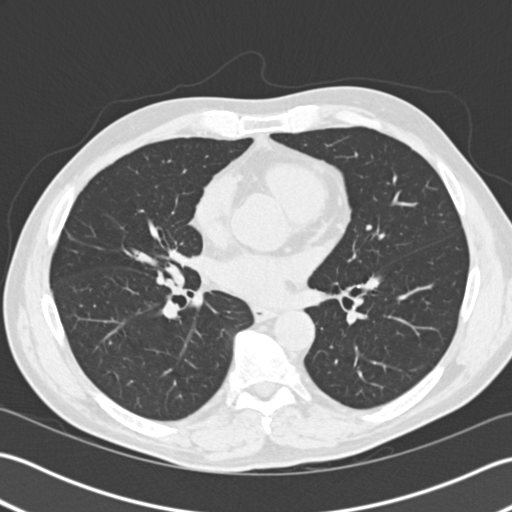
Chest CT (low-dose screening protocol), one axial image. Second screening round (one year after baseline). Lung window (W 1500 / L -600 HU). Slice 102 of 192 in the series. 512 × 512 image matrix. Male participant, aged 57 years at enrolment. Former smoker at enrolment.
Lesion marked by an expert reader, bounding box <153,249,197,295> (left, top, right, bottom; pixels). No non-calcified nodule or mass ≥4 mm was recorded by the screening reader at this exam. Official screen result: negative screen, significant abnormalities not suspicious for lung cancer. Lung cancer was diagnosed 483 days after this screen: carcinoid tumor, NOS, right middle lobe, carcinoid, stage not assessed, 15 mm at pathology.